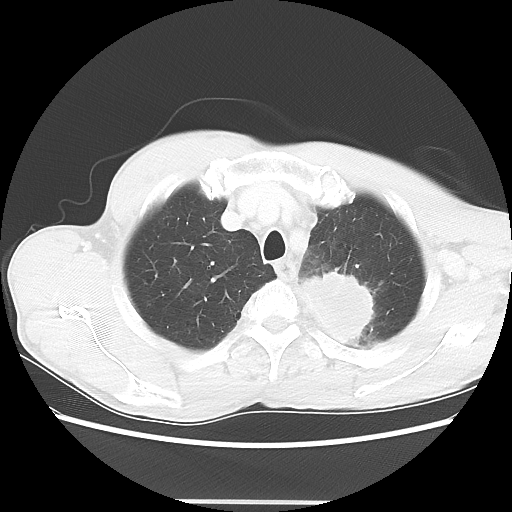
Chest CT, one axial slice; slice 54 of 62 in the series (ordered by position); reconstruction kernel LUNG; 100 kVp; lung window (W 1500 / L -600 HU); 512 × 512 image matrix. Patient: male, 61 years. Case-level facts recorded for this patient, not image findings: clinical TNM (as recorded): T3 N1 M1.
Structures marked on this image (rectangle marked by the reading radiologist):
- lung tumour (recorded histology: adenocarcinoma): bounding box [x1, y1, x2, y2] px = [295, 263, 376, 354]